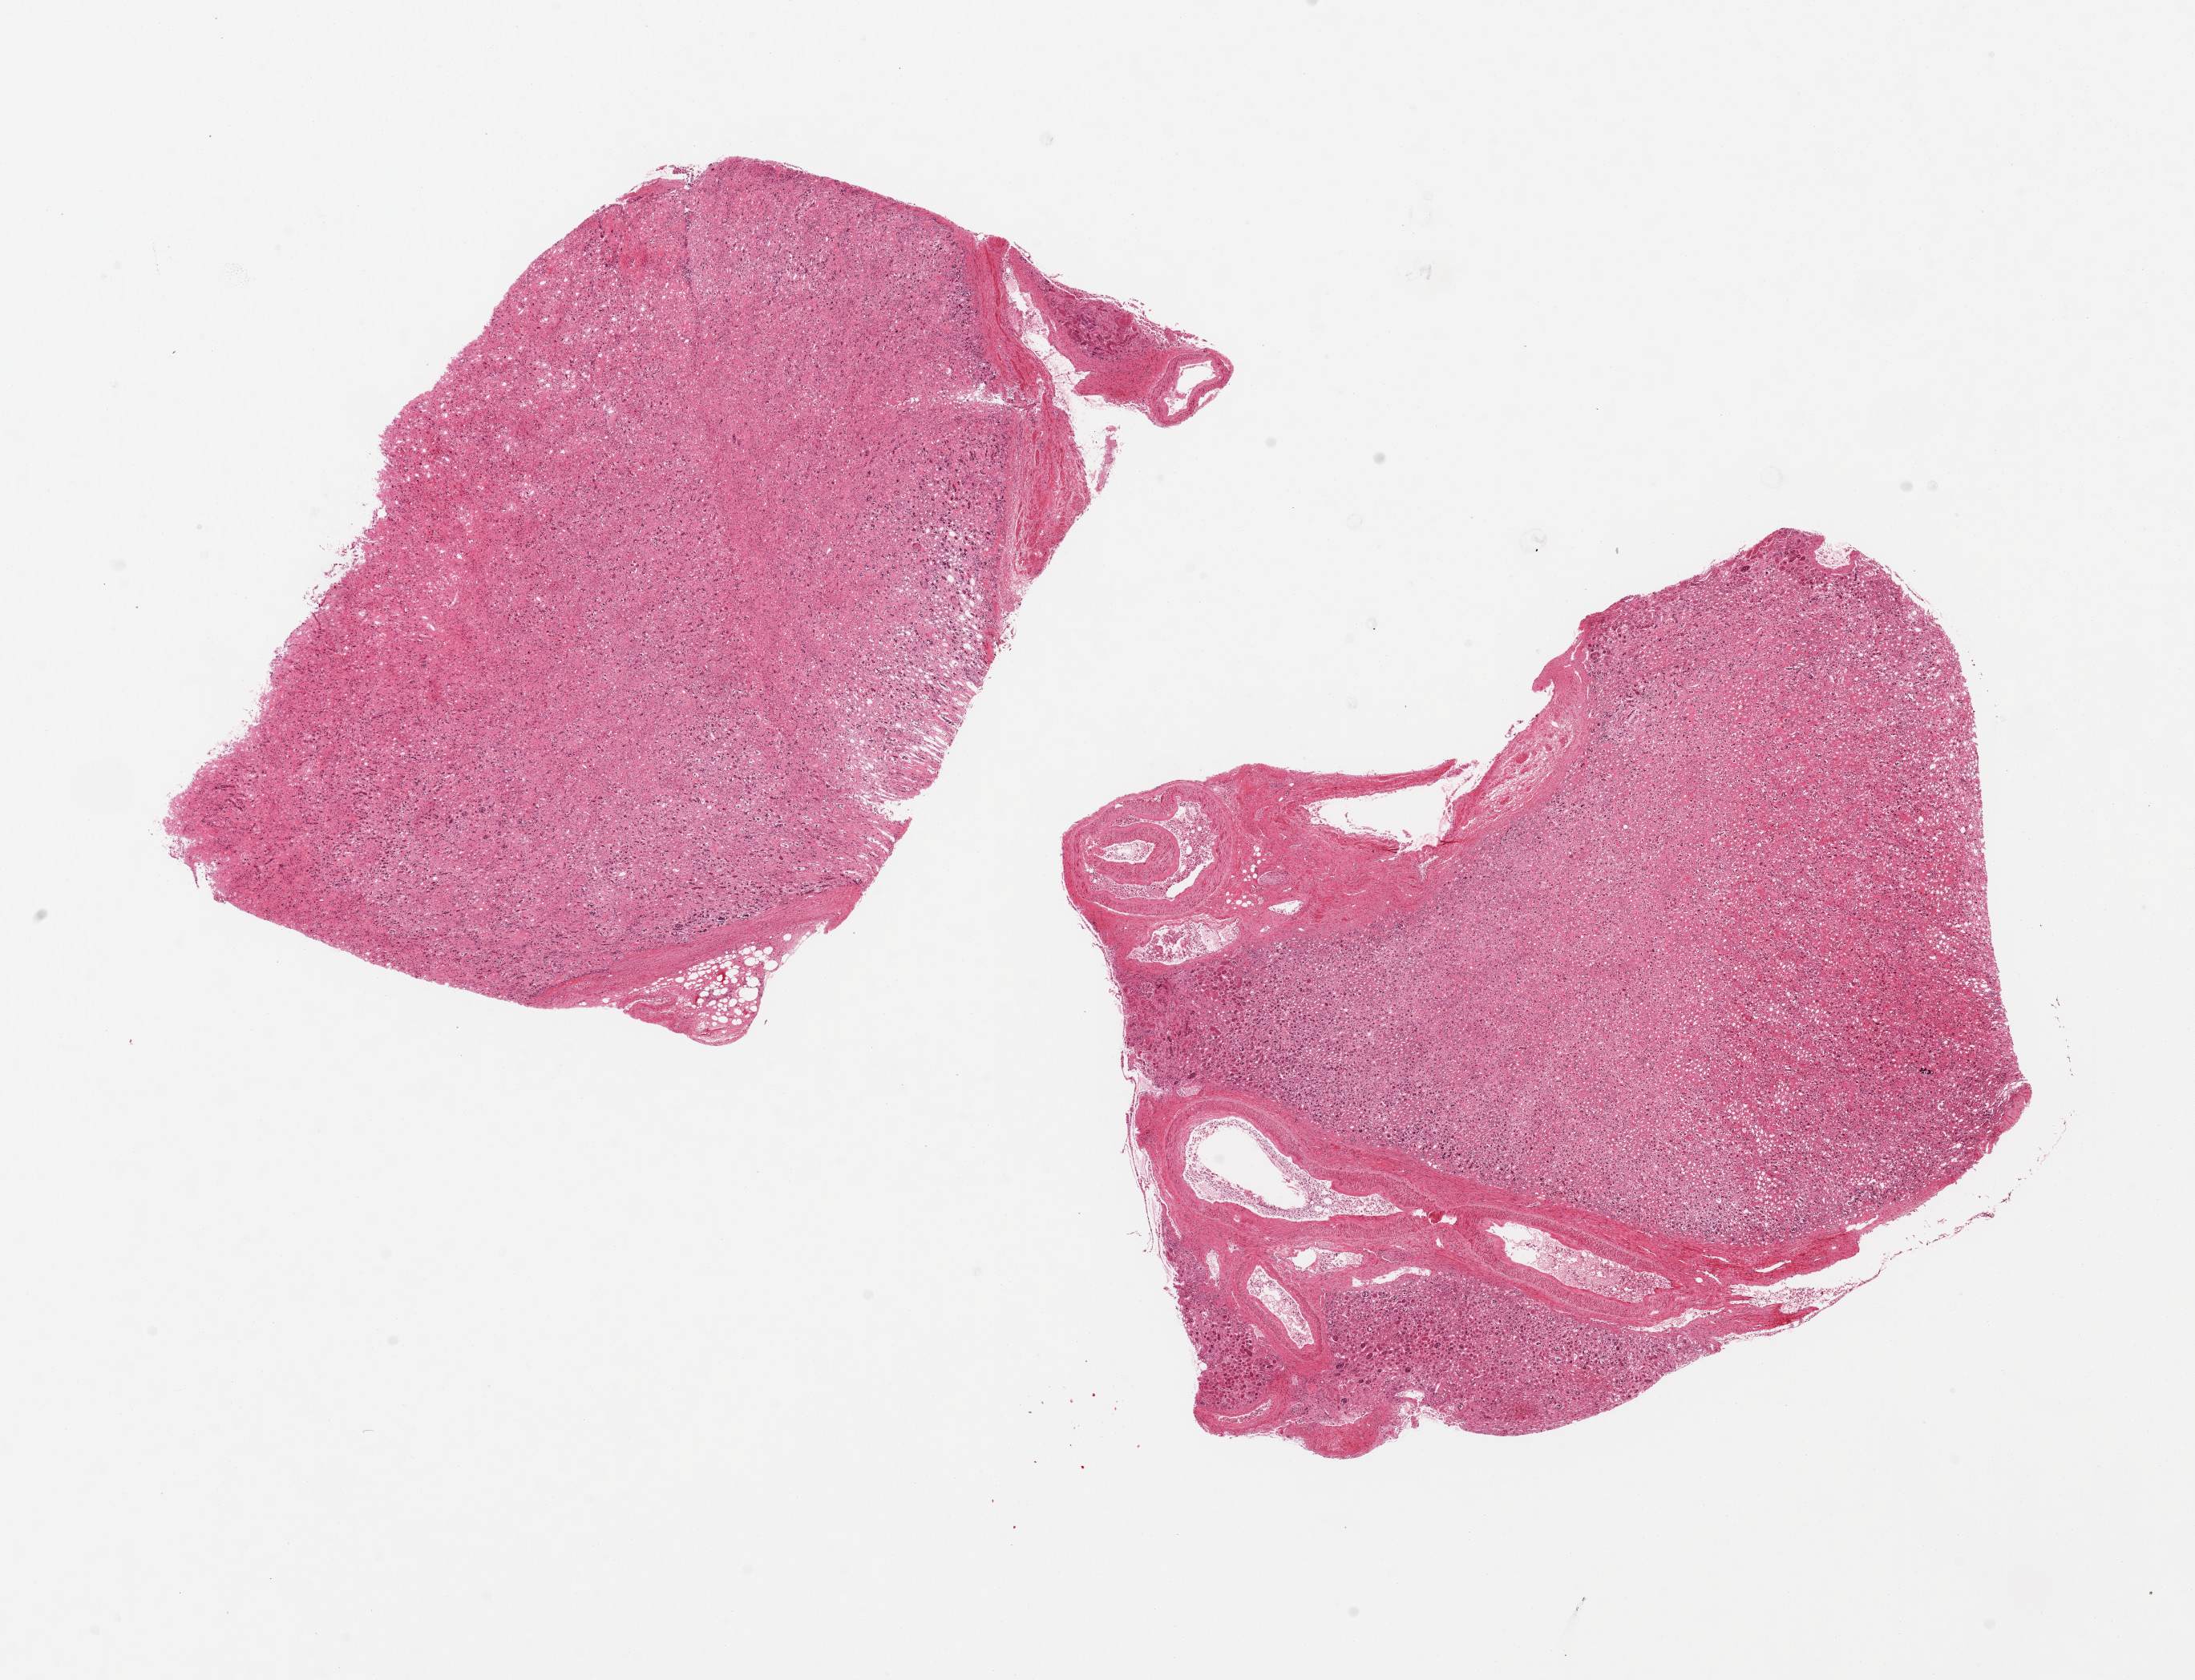
Digitized H&E-stained section, brightfield, shown as a low-resolution overview of the whole scanned area (about 21.7 x 16.6 mm); PAXgene-fixed, paraffin-embedded tissue; section of renal medulla (target tissue); donor tissue sample.
- reviewer comment on this tissue sample: 2 pieces 9x7 & 8x6 mm; all medulla no cortex